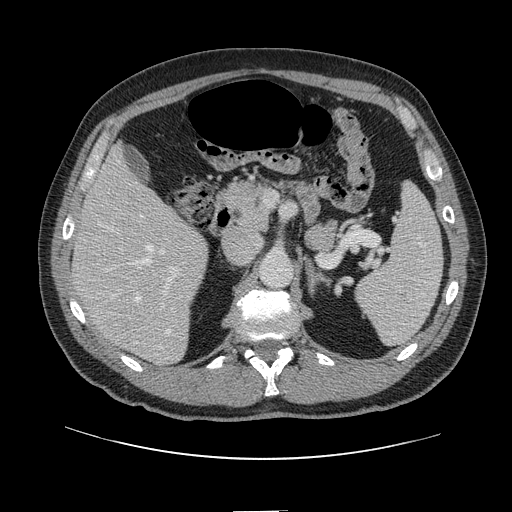
Contrast-enhanced abdominal CT, one axial slice; 120 kVp; intravenous contrast given; soft-tissue window (W 400 / L 40 HU); 2.5 mm slice thickness; 512 × 512 image matrix, field of view 412 × 412 mm. Male patient, age 66 years. Case-level facts recorded for this patient, not image findings: diagnosis: colorectal cancer liver metastases, imaged before liver resection; multiple liver metastases: no; largest metastasis: 3.5 cm.
Structures marked on this image (outlined manually by an expert reader):
- hepatic veins: bounding box (x1, y1, x2, y2) in pixels: (118, 161, 170, 334)
- liver: (75, 150, 207, 364)
- planned liver remnant (the part of the liver to remain after resection): (75, 150, 184, 290)
- portal vein (with intrahepatic branches): (118, 213, 180, 310)